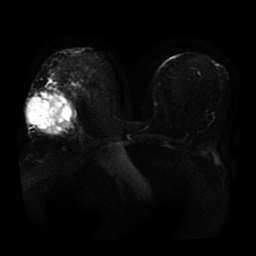
Breast MRI, one axial slice; position 26 of 41 along the scan axis; diffusion-weighted series; image 2 of 4 stored at this slice position (different b-values; order by instance number); 1.5 T; 5 mm slice thickness; 256 × 256 image matrix, field of view 360 × 360 mm. Female patient.
Annotated regions visible in this slice (manually delineated by an expert):
- tumour on diffusion-weighted imaging: bounding box <28,98,62,132> (left, top, right, bottom; pixels)